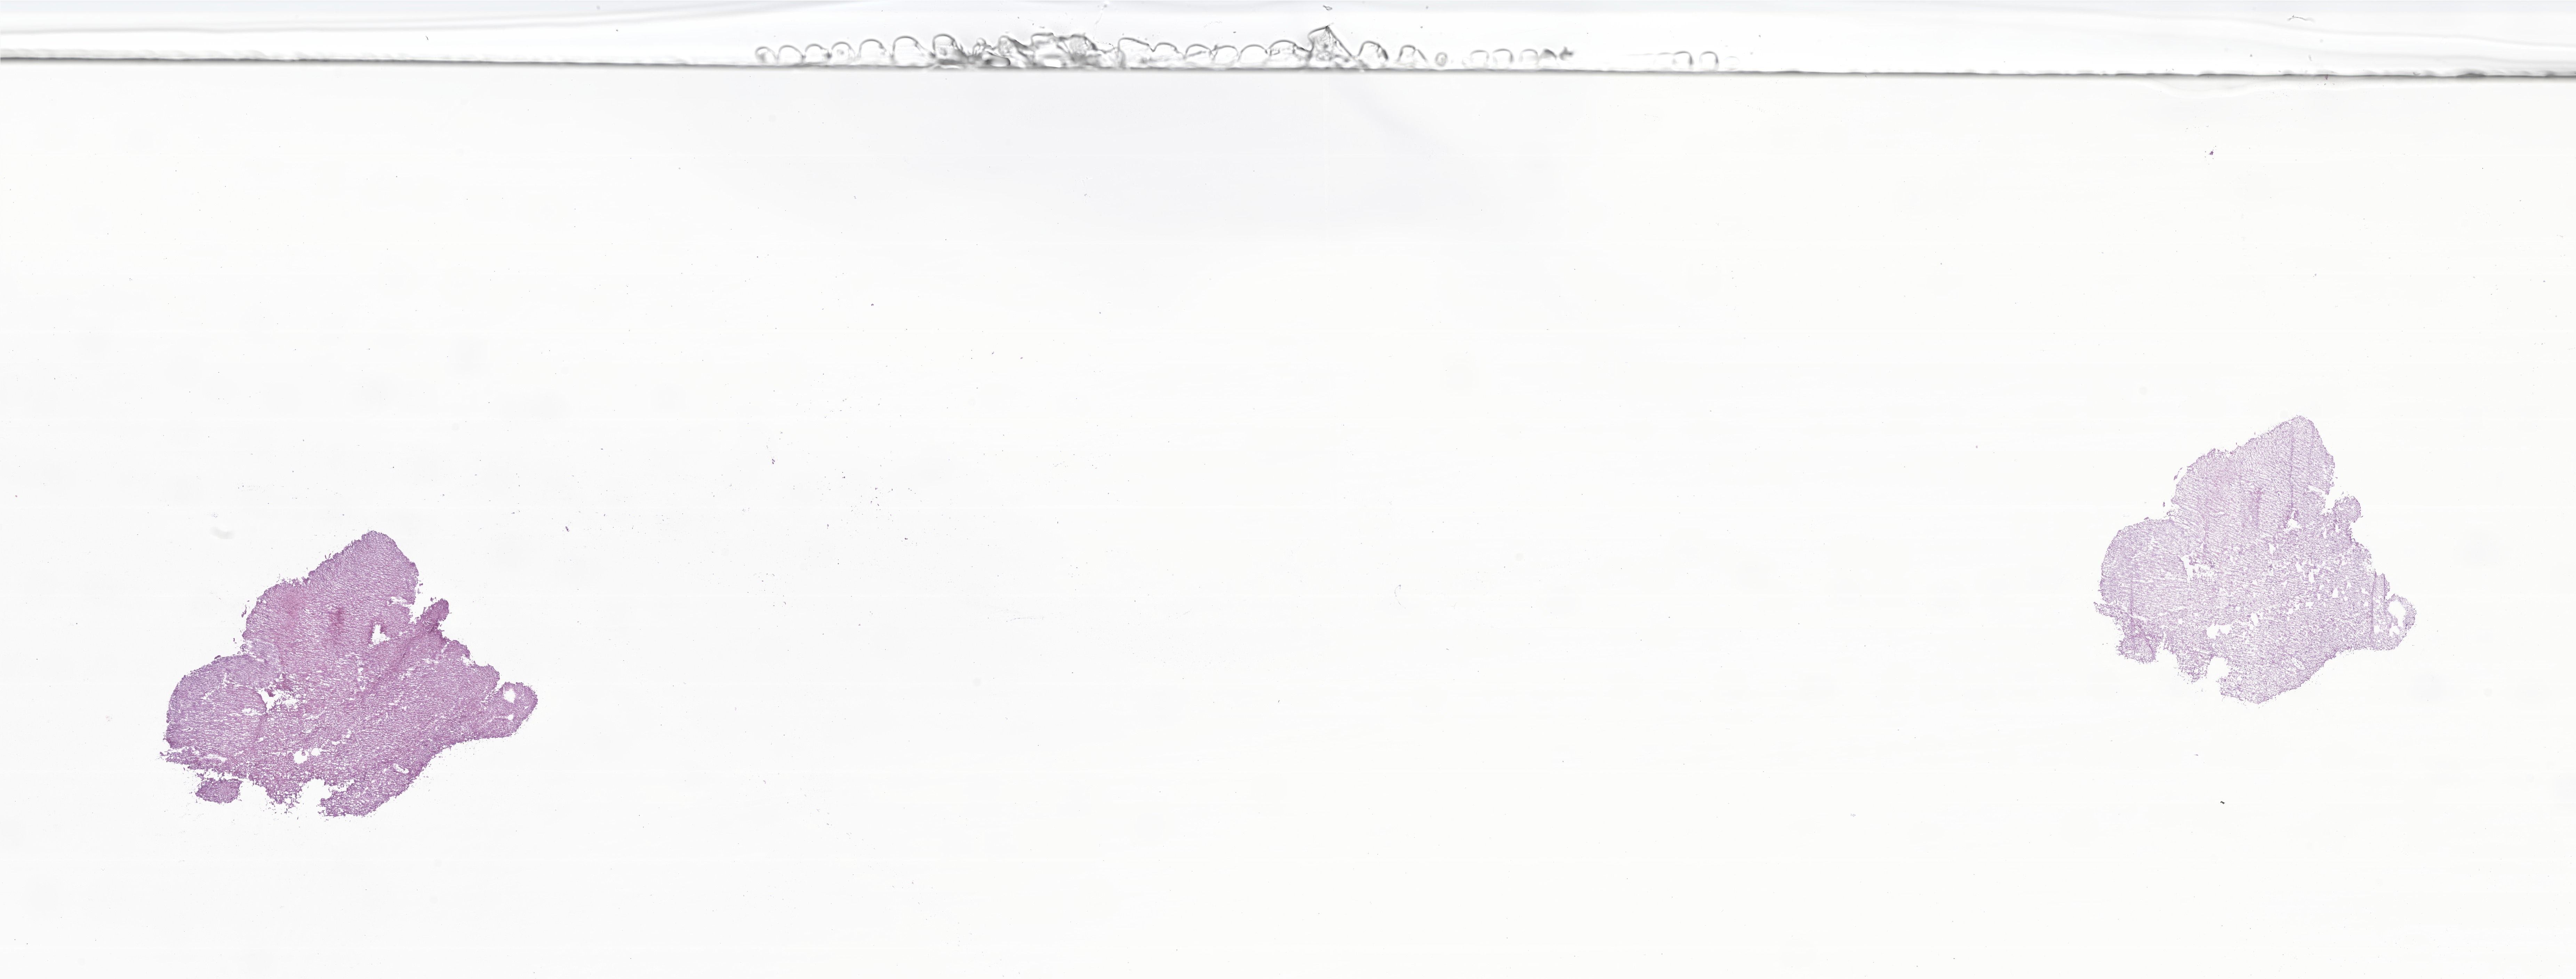
Digitized haematoxylin and eosin-stained section of tumor tissue from the brain — shown as a low-resolution overview of the whole scanned area (about 31.2 x 11.9 mm); frozen section (OCT-embedded). Male patient, age 208 months (17 years 4 months).
Recorded diagnosis: Glioma, malignant.